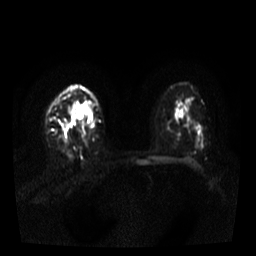
Breast MRI, one axial slice; position 22 of 37 along the scan axis; diffusion-weighted series; image 2 of 4 stored at this slice position (different b-values; order by instance number); 3 T; 5 mm slice thickness; 256 × 256 image matrix, field of view 320 × 320 mm. Female patient.
Structures marked on this image (outlined manually by an expert reader):
- tumour on diffusion-weighted imaging: bounding box <64,121,72,129> (left, top, right, bottom; pixels)